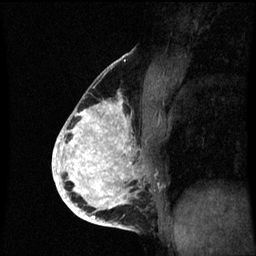
Breast MRI (dynamic contrast-enhanced), one sagittal slice. Slice 35 of 60 in the series (ordered by position). Dynamic contrast-enhanced series, image 2 of 3 at this slice position (ordered by acquisition). 1.5 T. TE 4.2 ms, TR 8.9 ms. 2 mm slice thickness. 256 × 256 image matrix, field of view 200 × 200 mm. Patient: female, 35 years. From the clinical record (not read from this slice): setting: breast cancer imaged before/during neoadjuvant chemotherapy; receptor status: HR-positive, HER2-negative.
Annotated regions visible in this slice (semi-automatically segmented with operator editing):
- analysis volume of interest (the breast-tissue region the enhancement analysis was run in; not a lesion): bounding box [x1, y1, x2, y2] px = [66, 100, 152, 215]
- tumour enhancement mask (voxels above the 70 % enhancement threshold inside the analysis volume of interest): [66, 102, 131, 215]